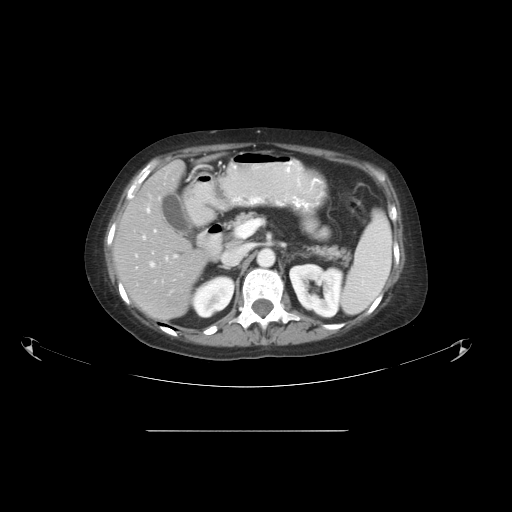
Contrast-enhanced abdominal CT, one axial slice. Slice 30 of 51 in the series (ordered by position). Reconstruction kernel STANDARD. Intravenous contrast given. Soft-tissue window (W 400 / L 40 HU). 5 mm slice thickness. 512 × 512 image matrix, field of view 475 × 475 mm. Female patient, age 48 years. Case-level facts recorded for this patient, not image findings: diagnosis: colorectal cancer liver metastases, imaged before liver resection; multiple liver metastases: yes; largest metastasis: 1 cm; disease in both lobes: no.
Structures marked on this image (manually delineated by an expert):
- hepatic veins: bounding box [x1, y1, x2, y2] px = [150, 198, 177, 267]
- liver: [115, 163, 210, 321]
- planned liver remnant (the part of the liver to remain after resection): [115, 162, 211, 321]
- portal vein (with intrahepatic branches): [135, 208, 156, 269]